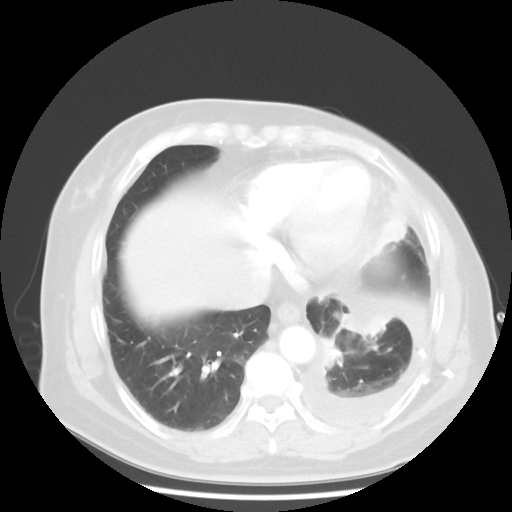
Chest CT, one axial slice. Reconstruction kernel STANDARD. Lung window (W 1500 / L -600 HU). 512 × 512 image matrix, field of view 360 × 360 mm. Patient: female, 63 years. Case-level facts recorded for this patient, not image findings: clinical TNM (as recorded): T2 N0 M1.
Structures marked on this image (rectangle marked by the reading radiologist):
- lung tumour (recorded histology: adenocarcinoma): box from (x=325, y=289) to (x=392, y=342) px